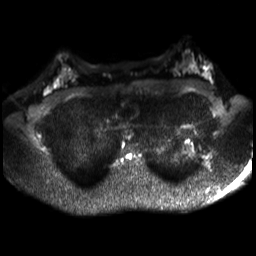
Breast MRI, one axial slice. Slice 21 of 30 in the series (ordered by position). Diffusion-weighted series; image 2 of 4 stored at this slice position (different b-values; order by instance number). 3 T. 4 mm slice thickness. 256 × 256 image matrix. Female patient.
Structures marked on this image (expert manual segmentation):
- tumour on diffusion-weighted imaging: bounding box (x1, y1, x2, y2) in pixels: (206, 65, 210, 76)